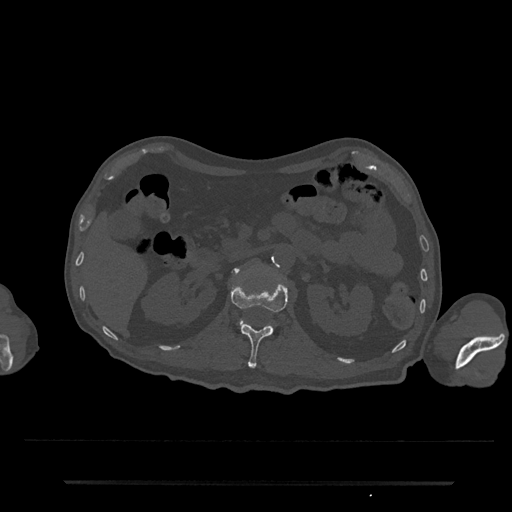
CT including the spine, one axial slice; slice 112 of 797 in the series (ordered by position); reconstruction kernel Br40s/3; 120 kVp; bone window (W 1800 / L 400 HU); 0.5 mm slice thickness; 512 × 512 image matrix, field of view 427 × 427 mm. Male patient, age 74 years. From the clinical record (not read from this slice): primary cancer: prostate.
Structures marked on this image (semi-automatic segmentation, software-assisted and operator-edited):
- L1 vertebra: bounding box [x1, y1, x2, y2] px = [231, 282, 288, 369]
- L2 vertebra: [240, 322, 243, 327]